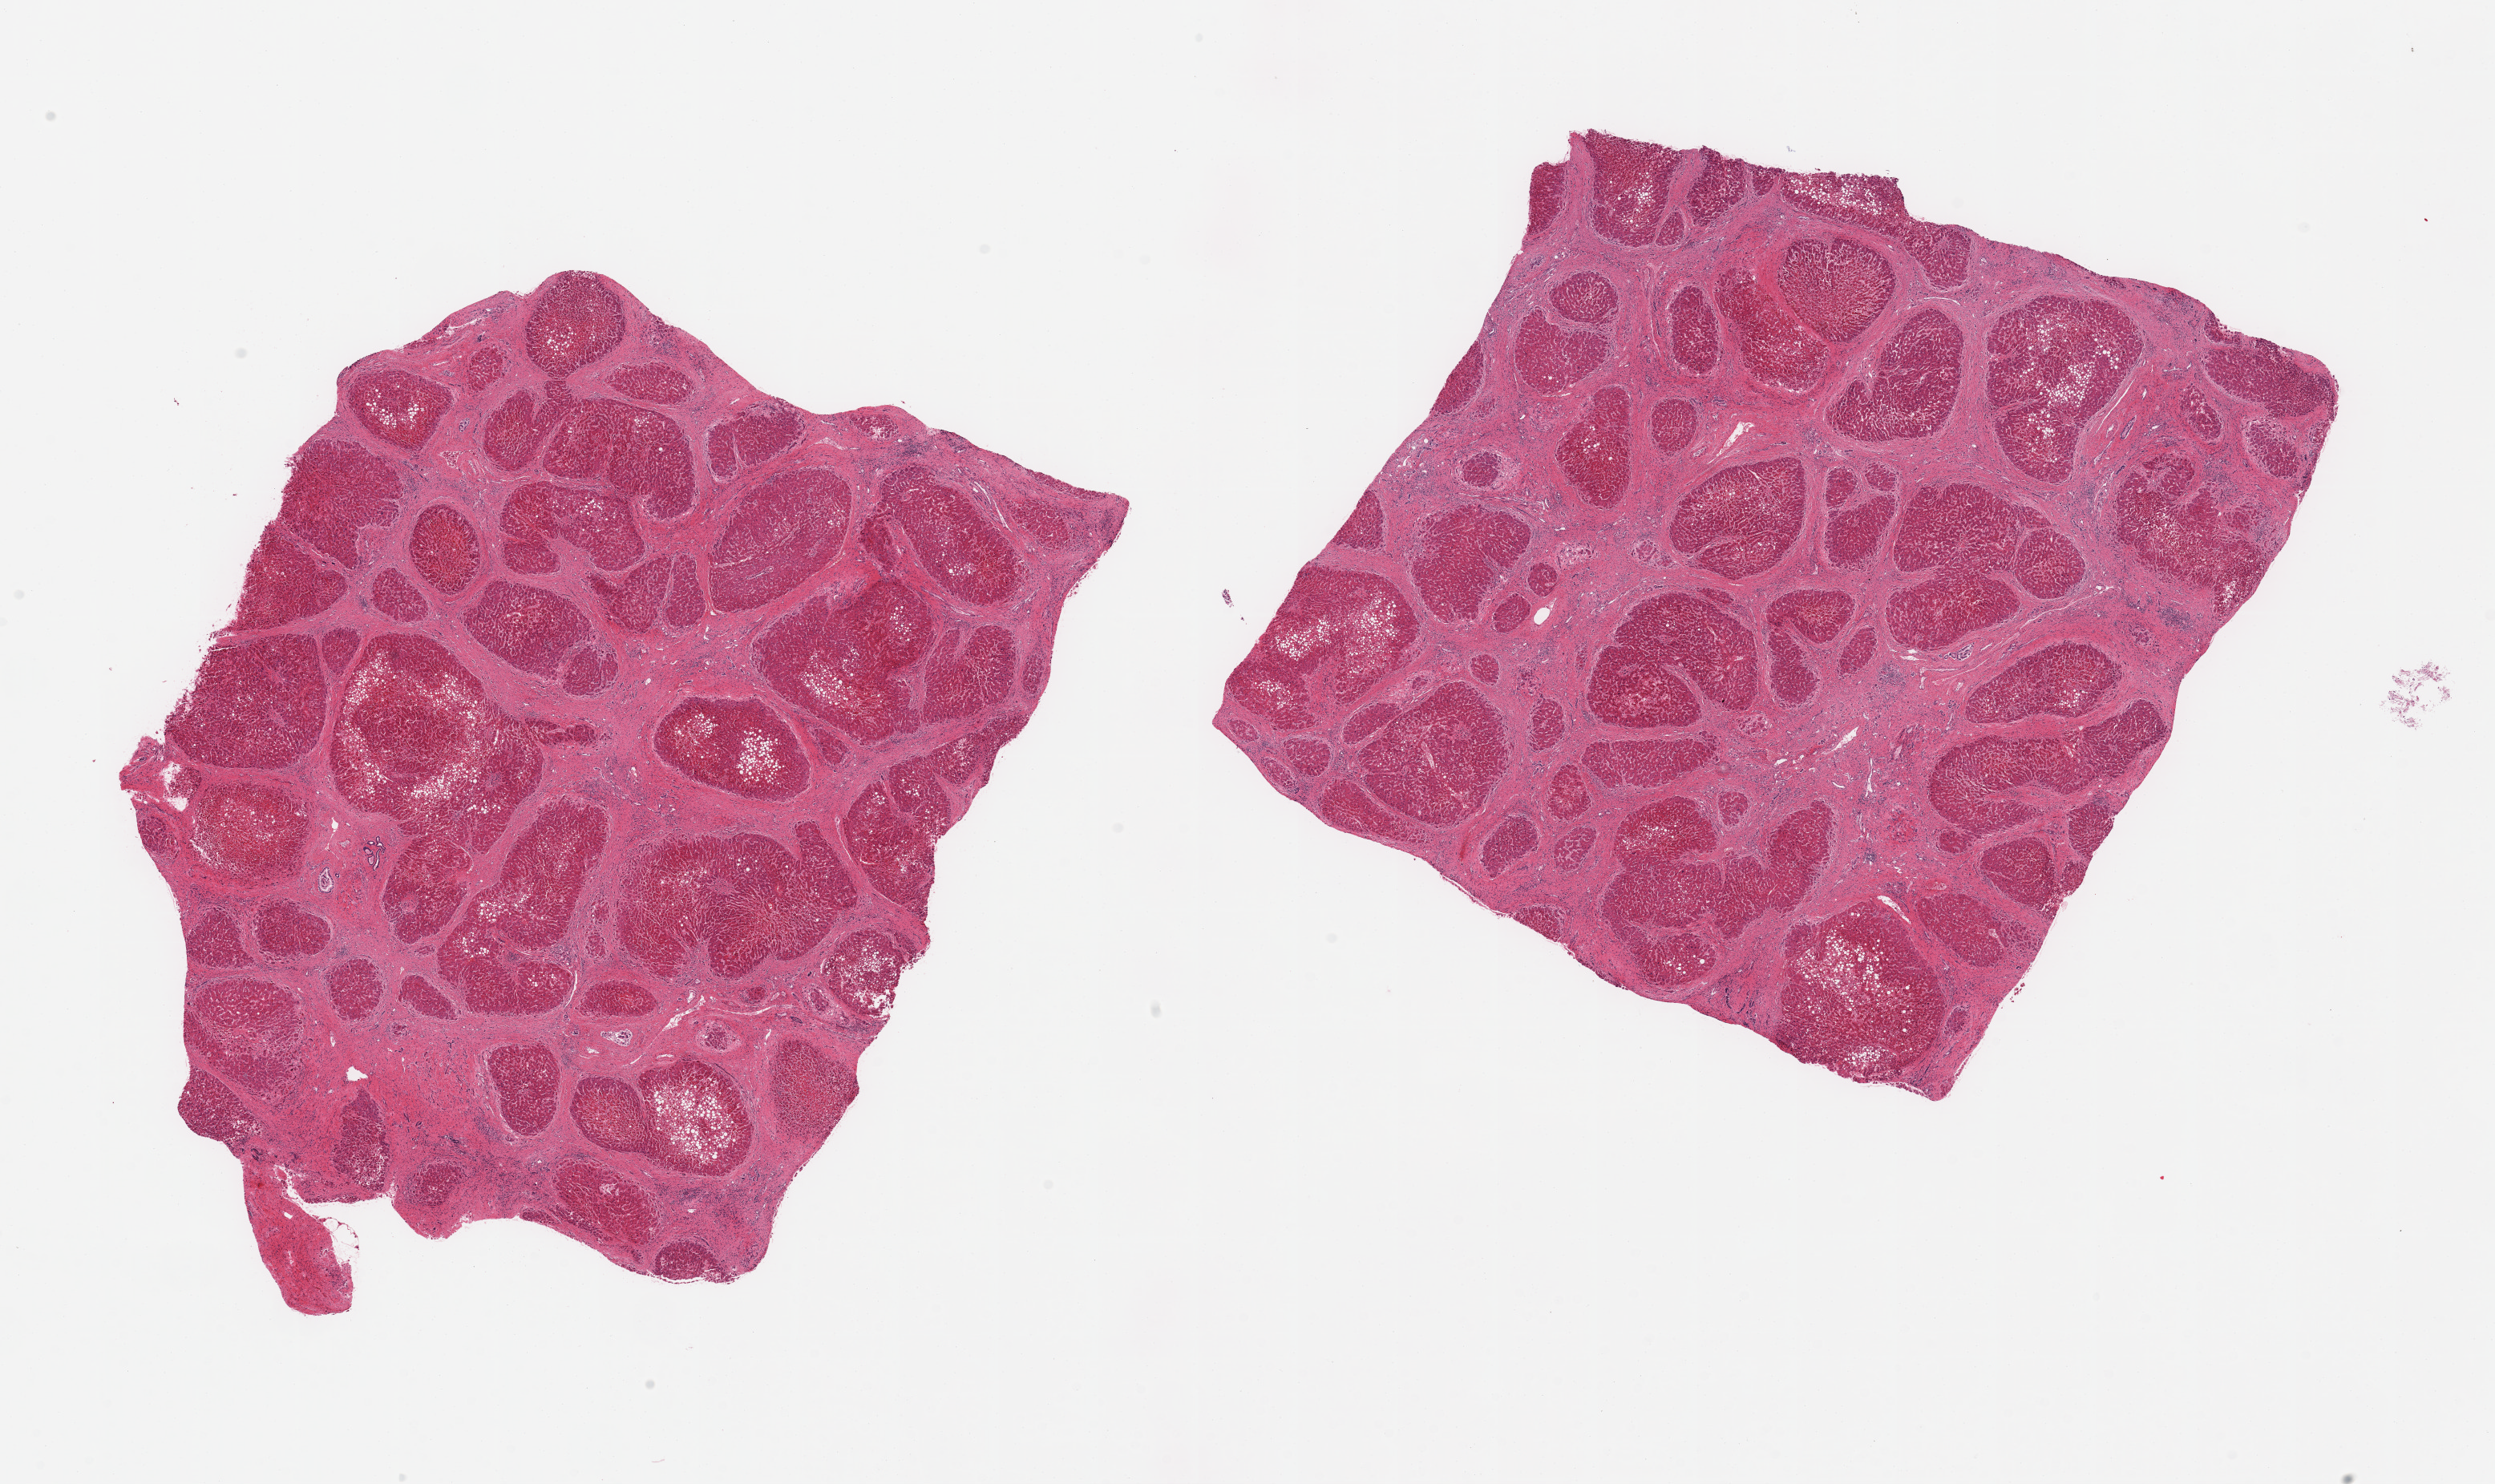
Whole-slide image, hematoxylin and eosin (H&E) stain — whole scanned area (about 24.6 x 14.6 mm) shown as a low-resolution overview; PAXgene-fixed, paraffin-embedded tissue; target tissue: liver; donor tissue sample. Donor sex: male.
- reviewer comment on this tissue sample: 2 pieces, advanced cirrhosis